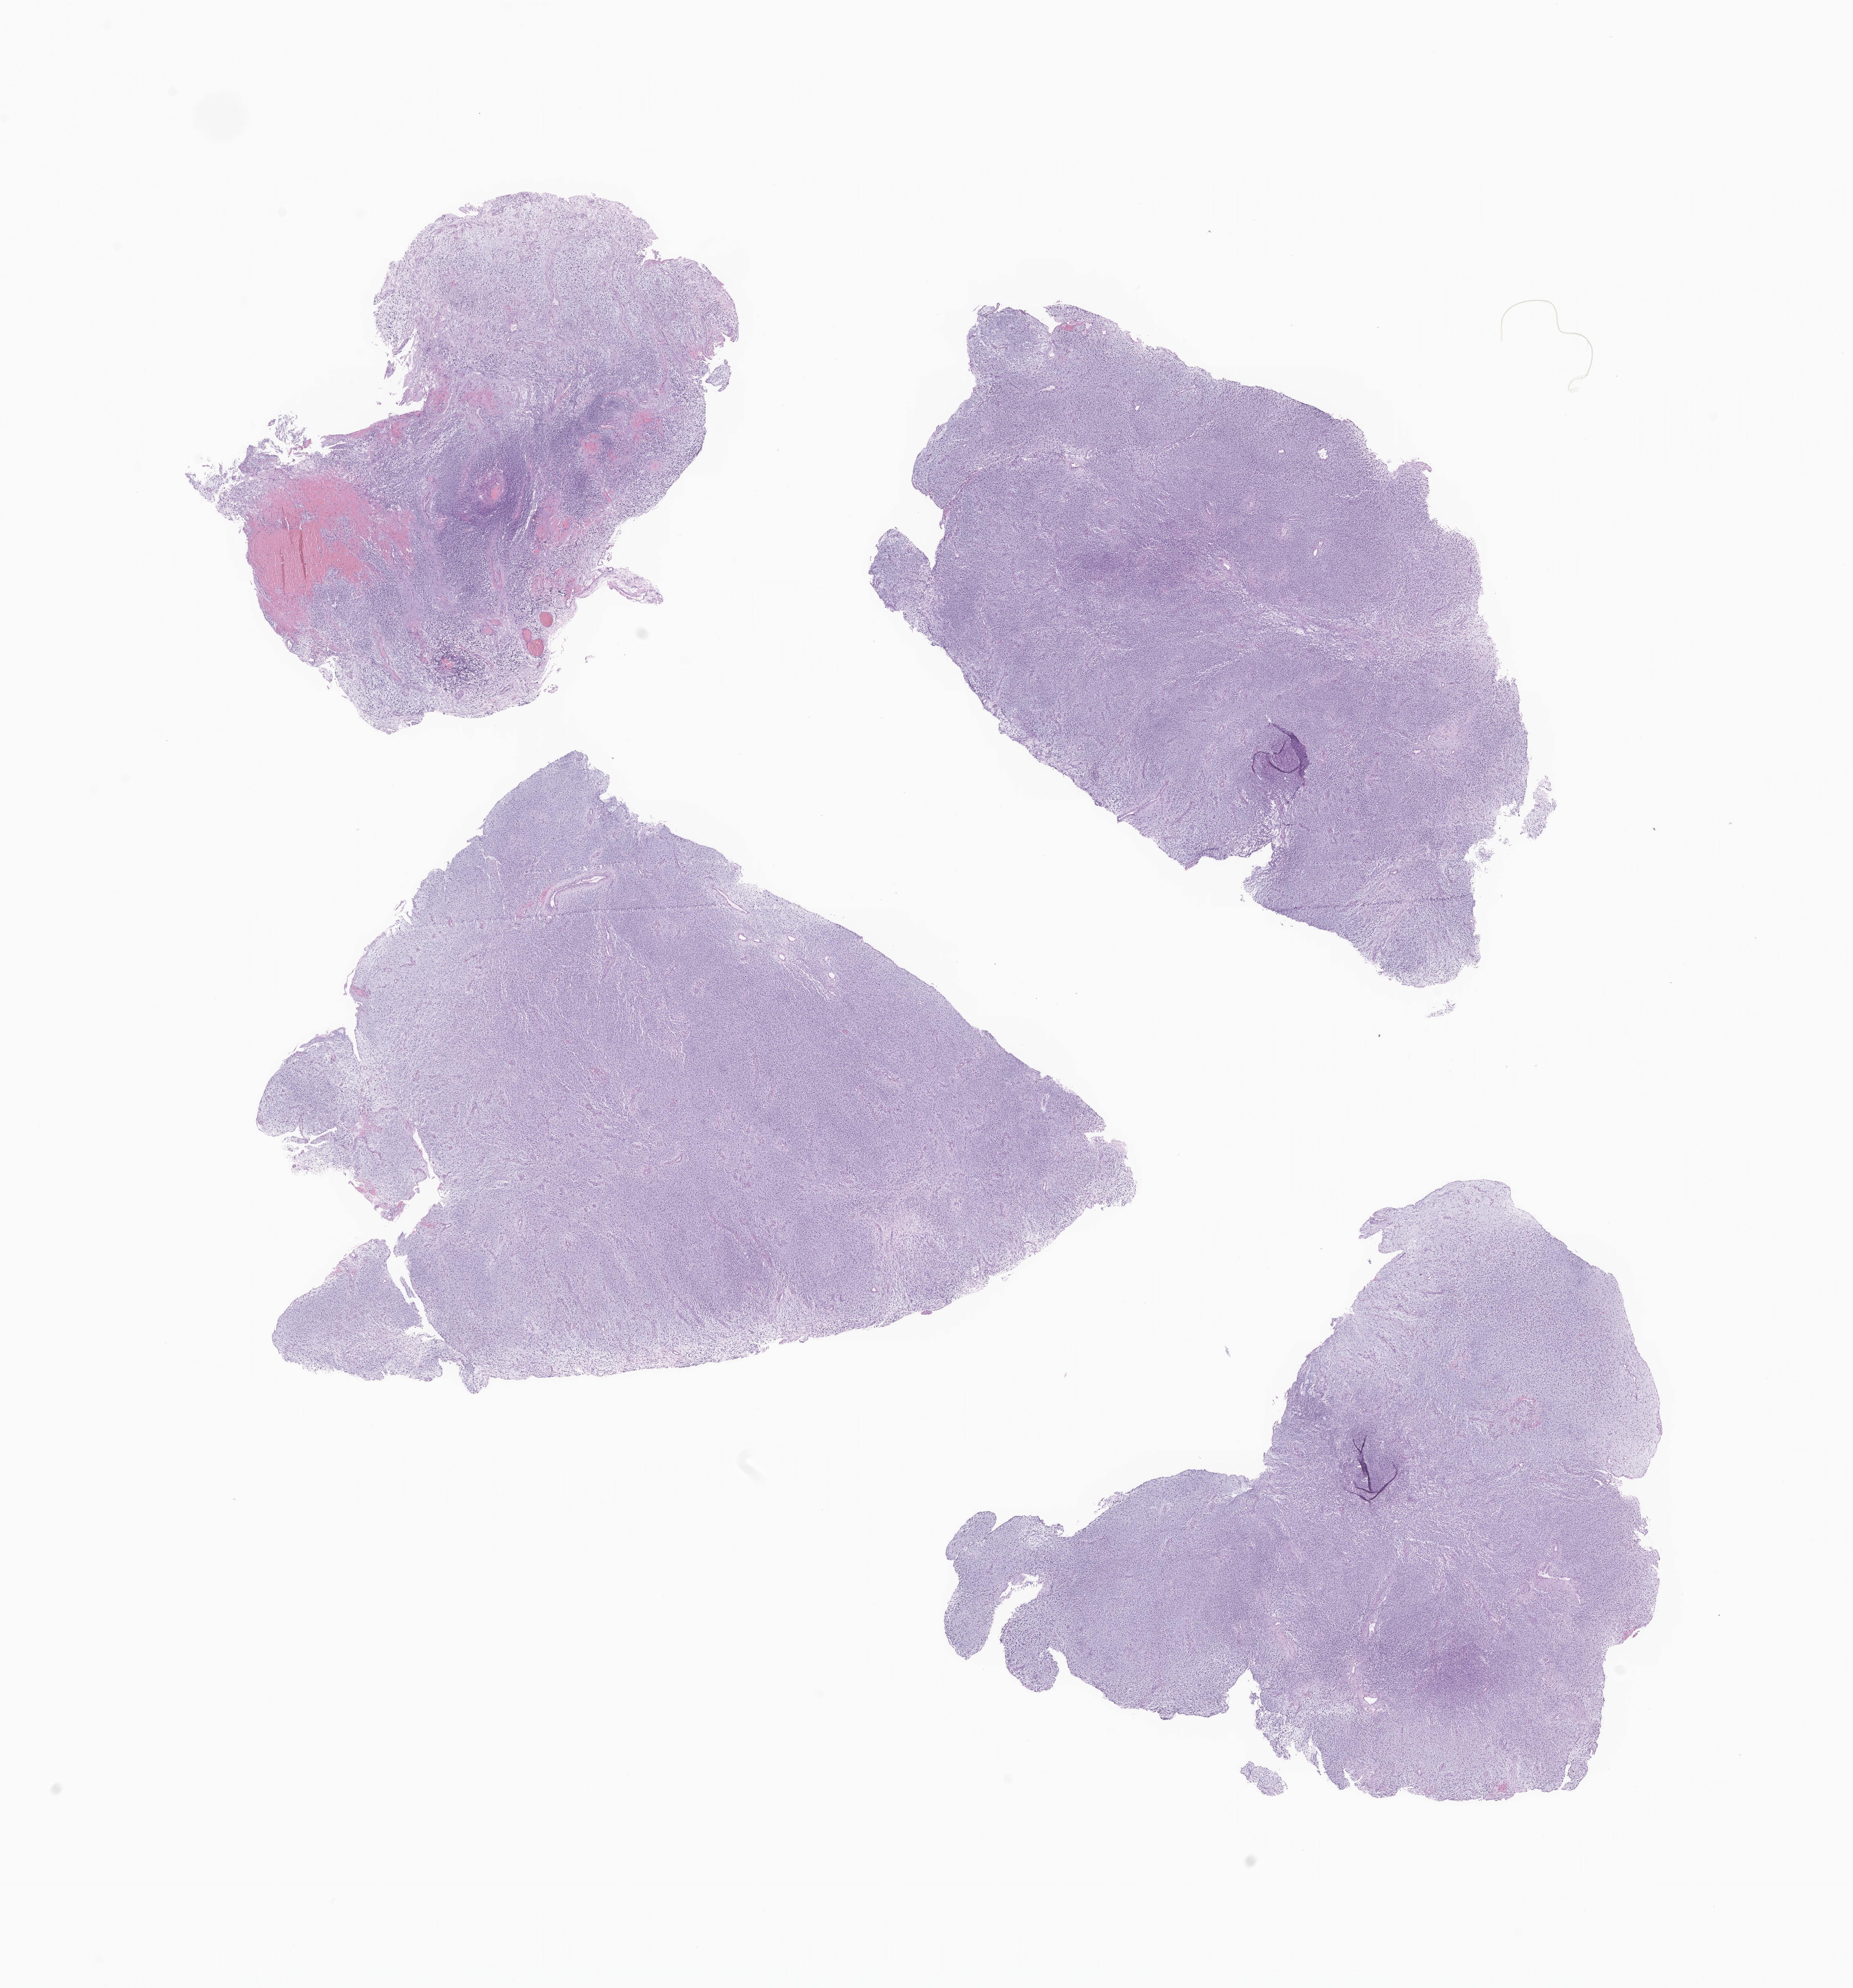
Digitized haematoxylin and eosin-stained section of tumor tissue from the orbit — shown as a low-resolution overview of the whole scanned area (about 18.3 x 19.6 mm). FFPE section. Patient female; age 118 months (9 years 10 months).
Recorded diagnosis: Embryonal rhabdomyosarcoma, NOS.